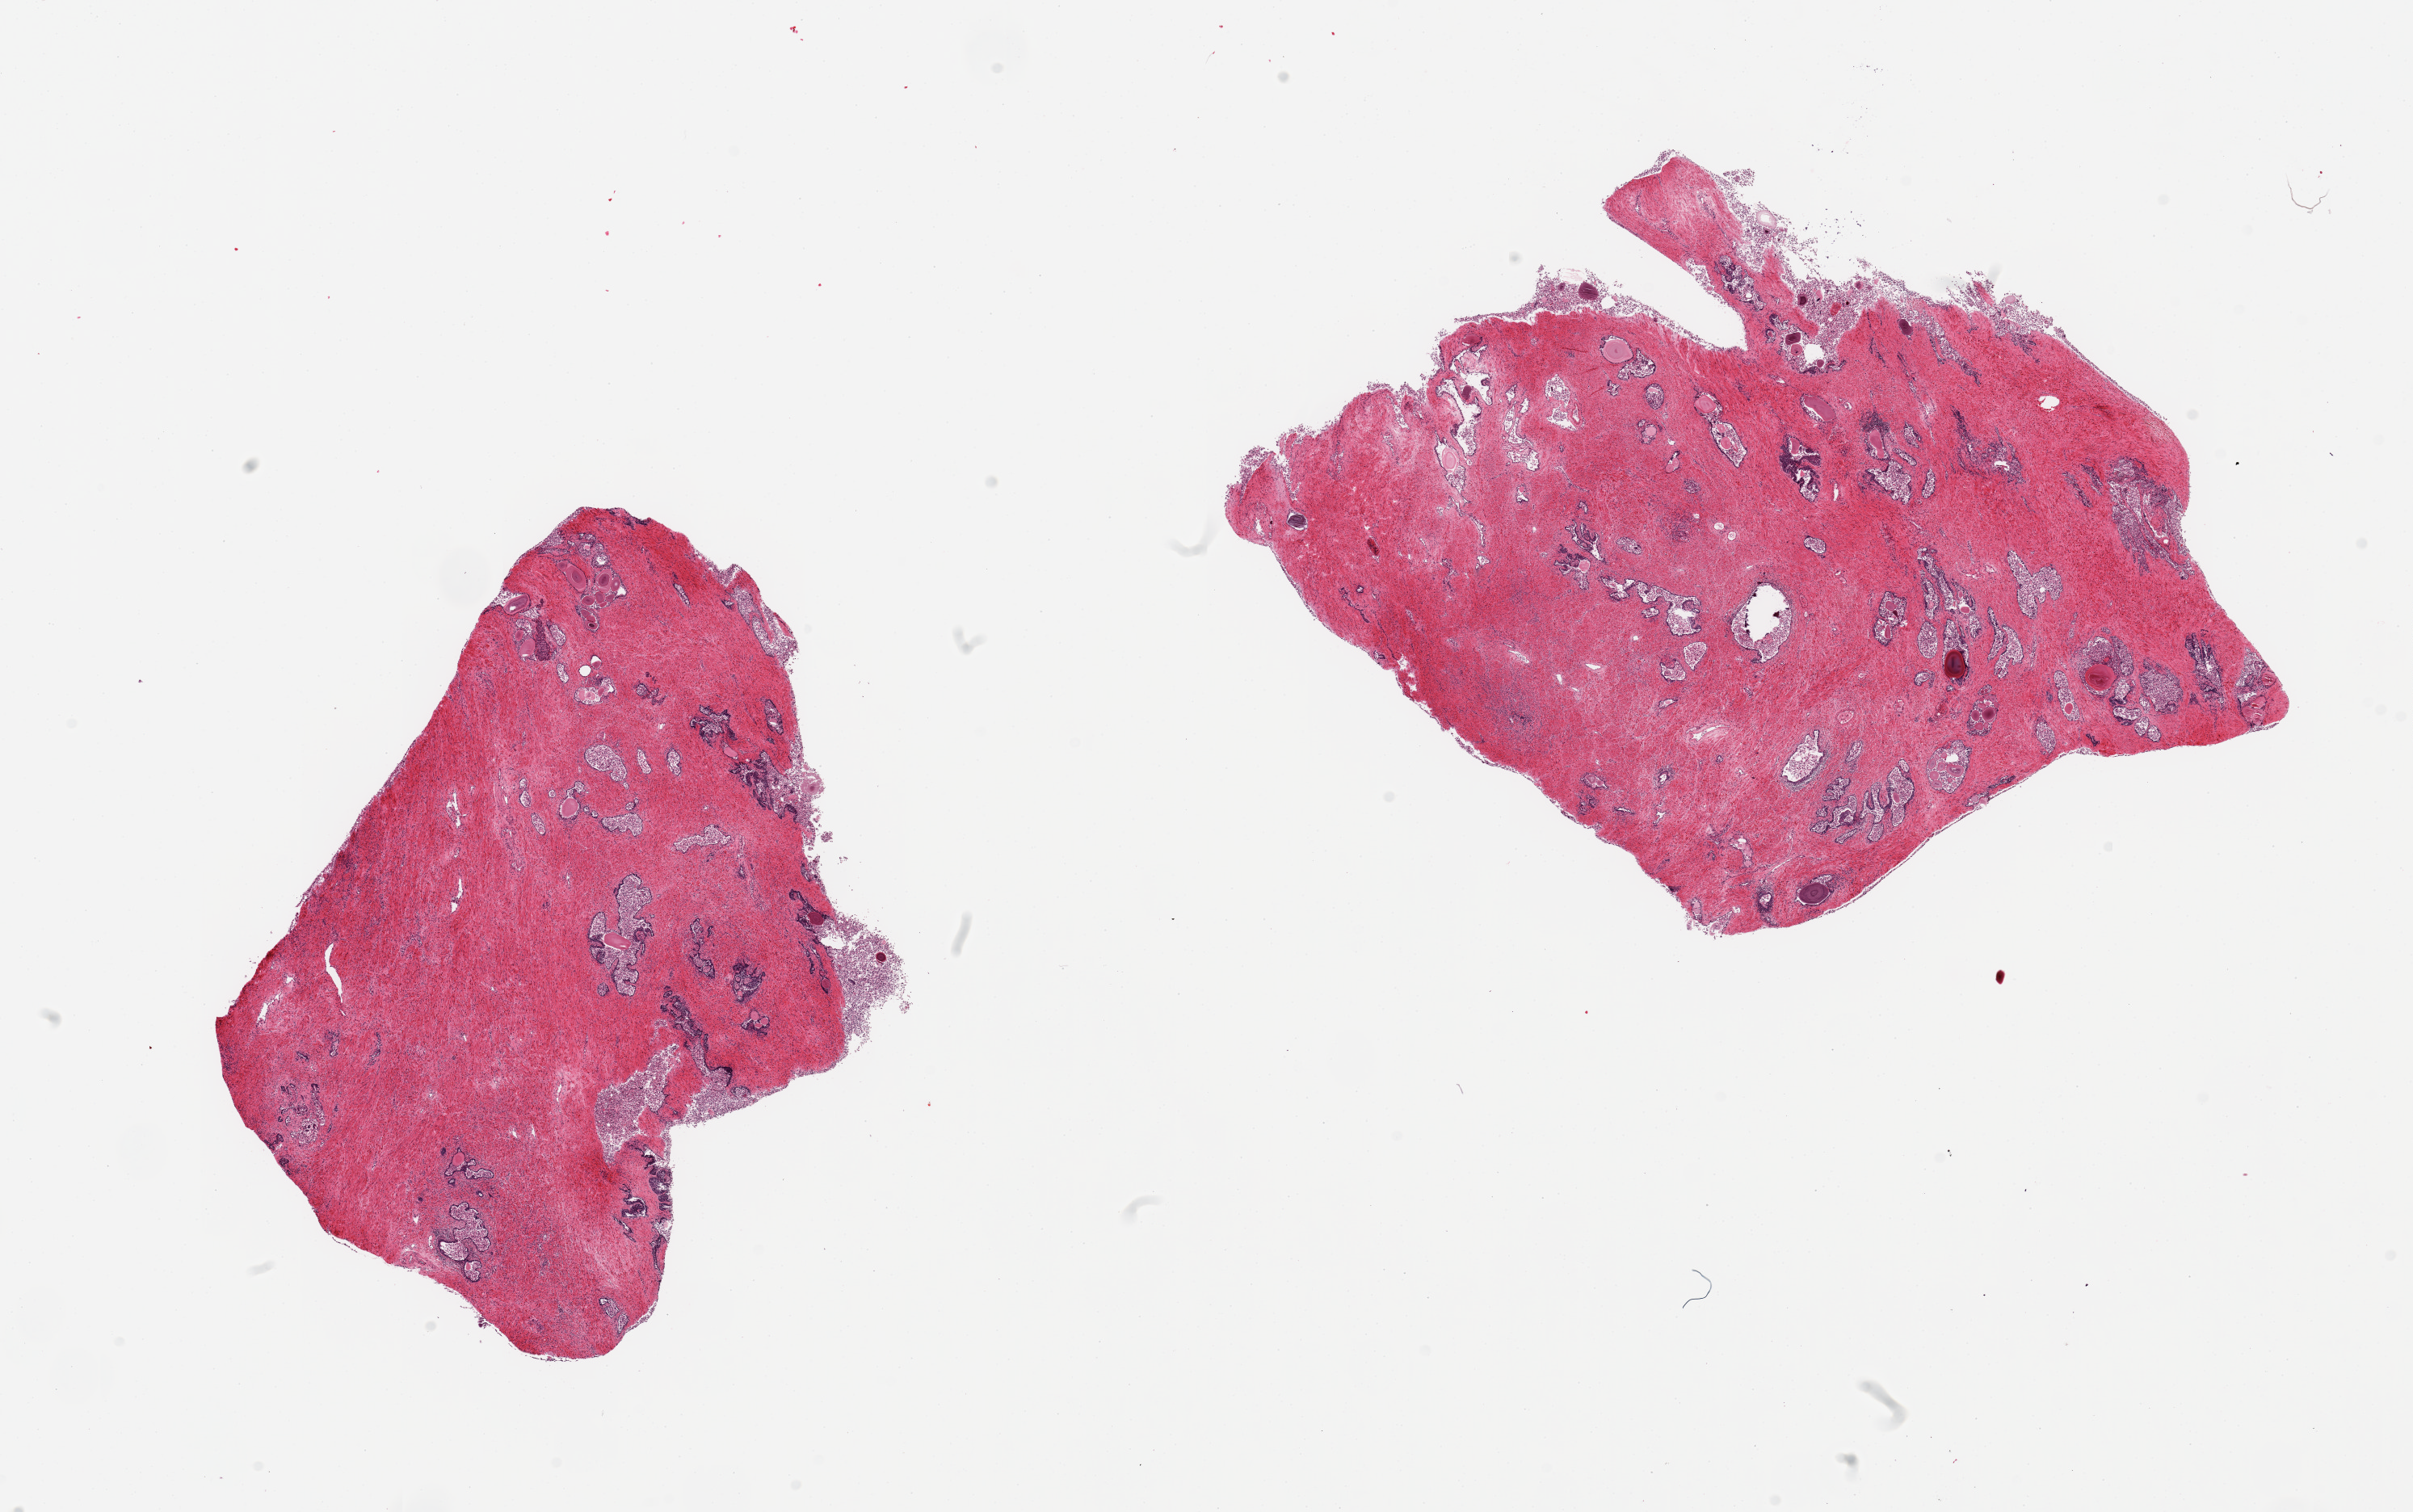
Hematoxylin and eosin (H&E) whole-slide image, brightfield, low-resolution overview of the scanned area, about 23.6 x 14.8 mm (from a 20x scan); PAXgene-fixed, paraffin-embedded tissue; target tissue: prostate; tissue donor sample. Donor: male.
* reviewer comment on this tissue sample: 2 pieces; sloughed glandular epithelium, numerous corpora amylacea